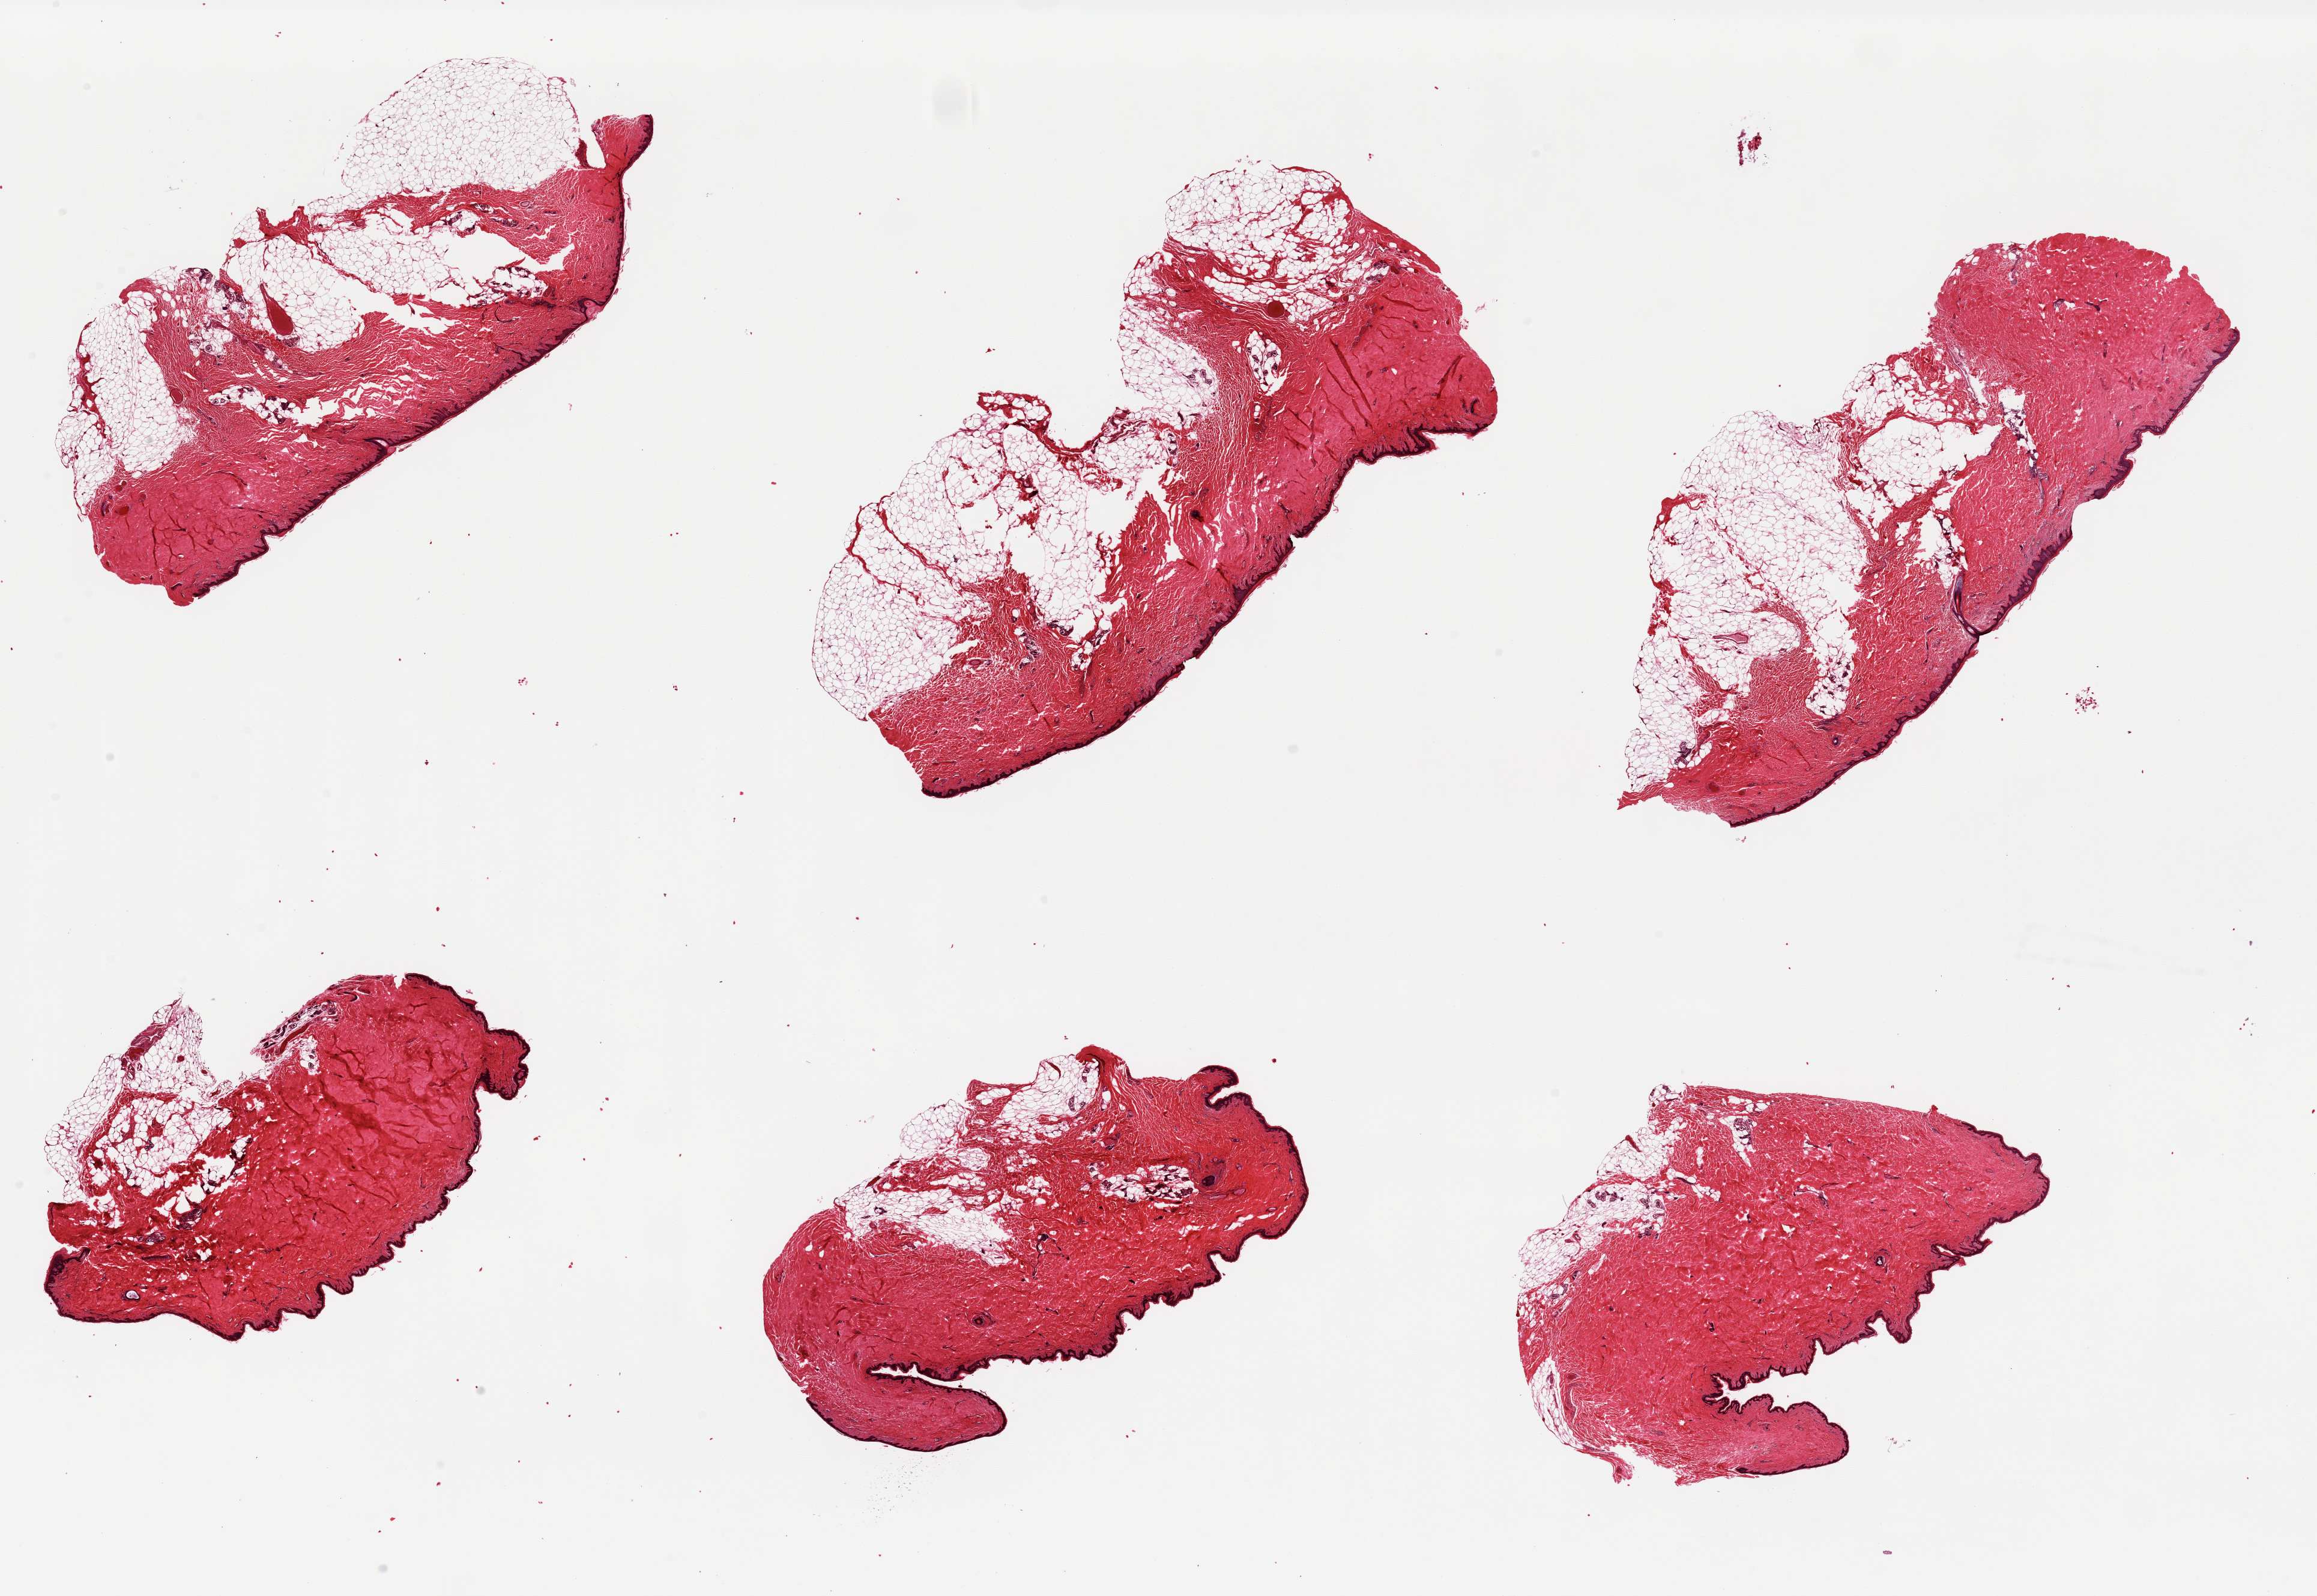
Digitized H&E-stained section — a low-resolution overview of the entire scanned area, about 30.5 x 21.0 mm (acquisition: 20x scan). PAXgene-fixed, paraffin-embedded tissue. Target tissue: skin of suprapubic region. Donor tissue sample.
Review note (as recorded): 6 pieces; all with excessive subcutaneous fat, up to 2.9mm thick.